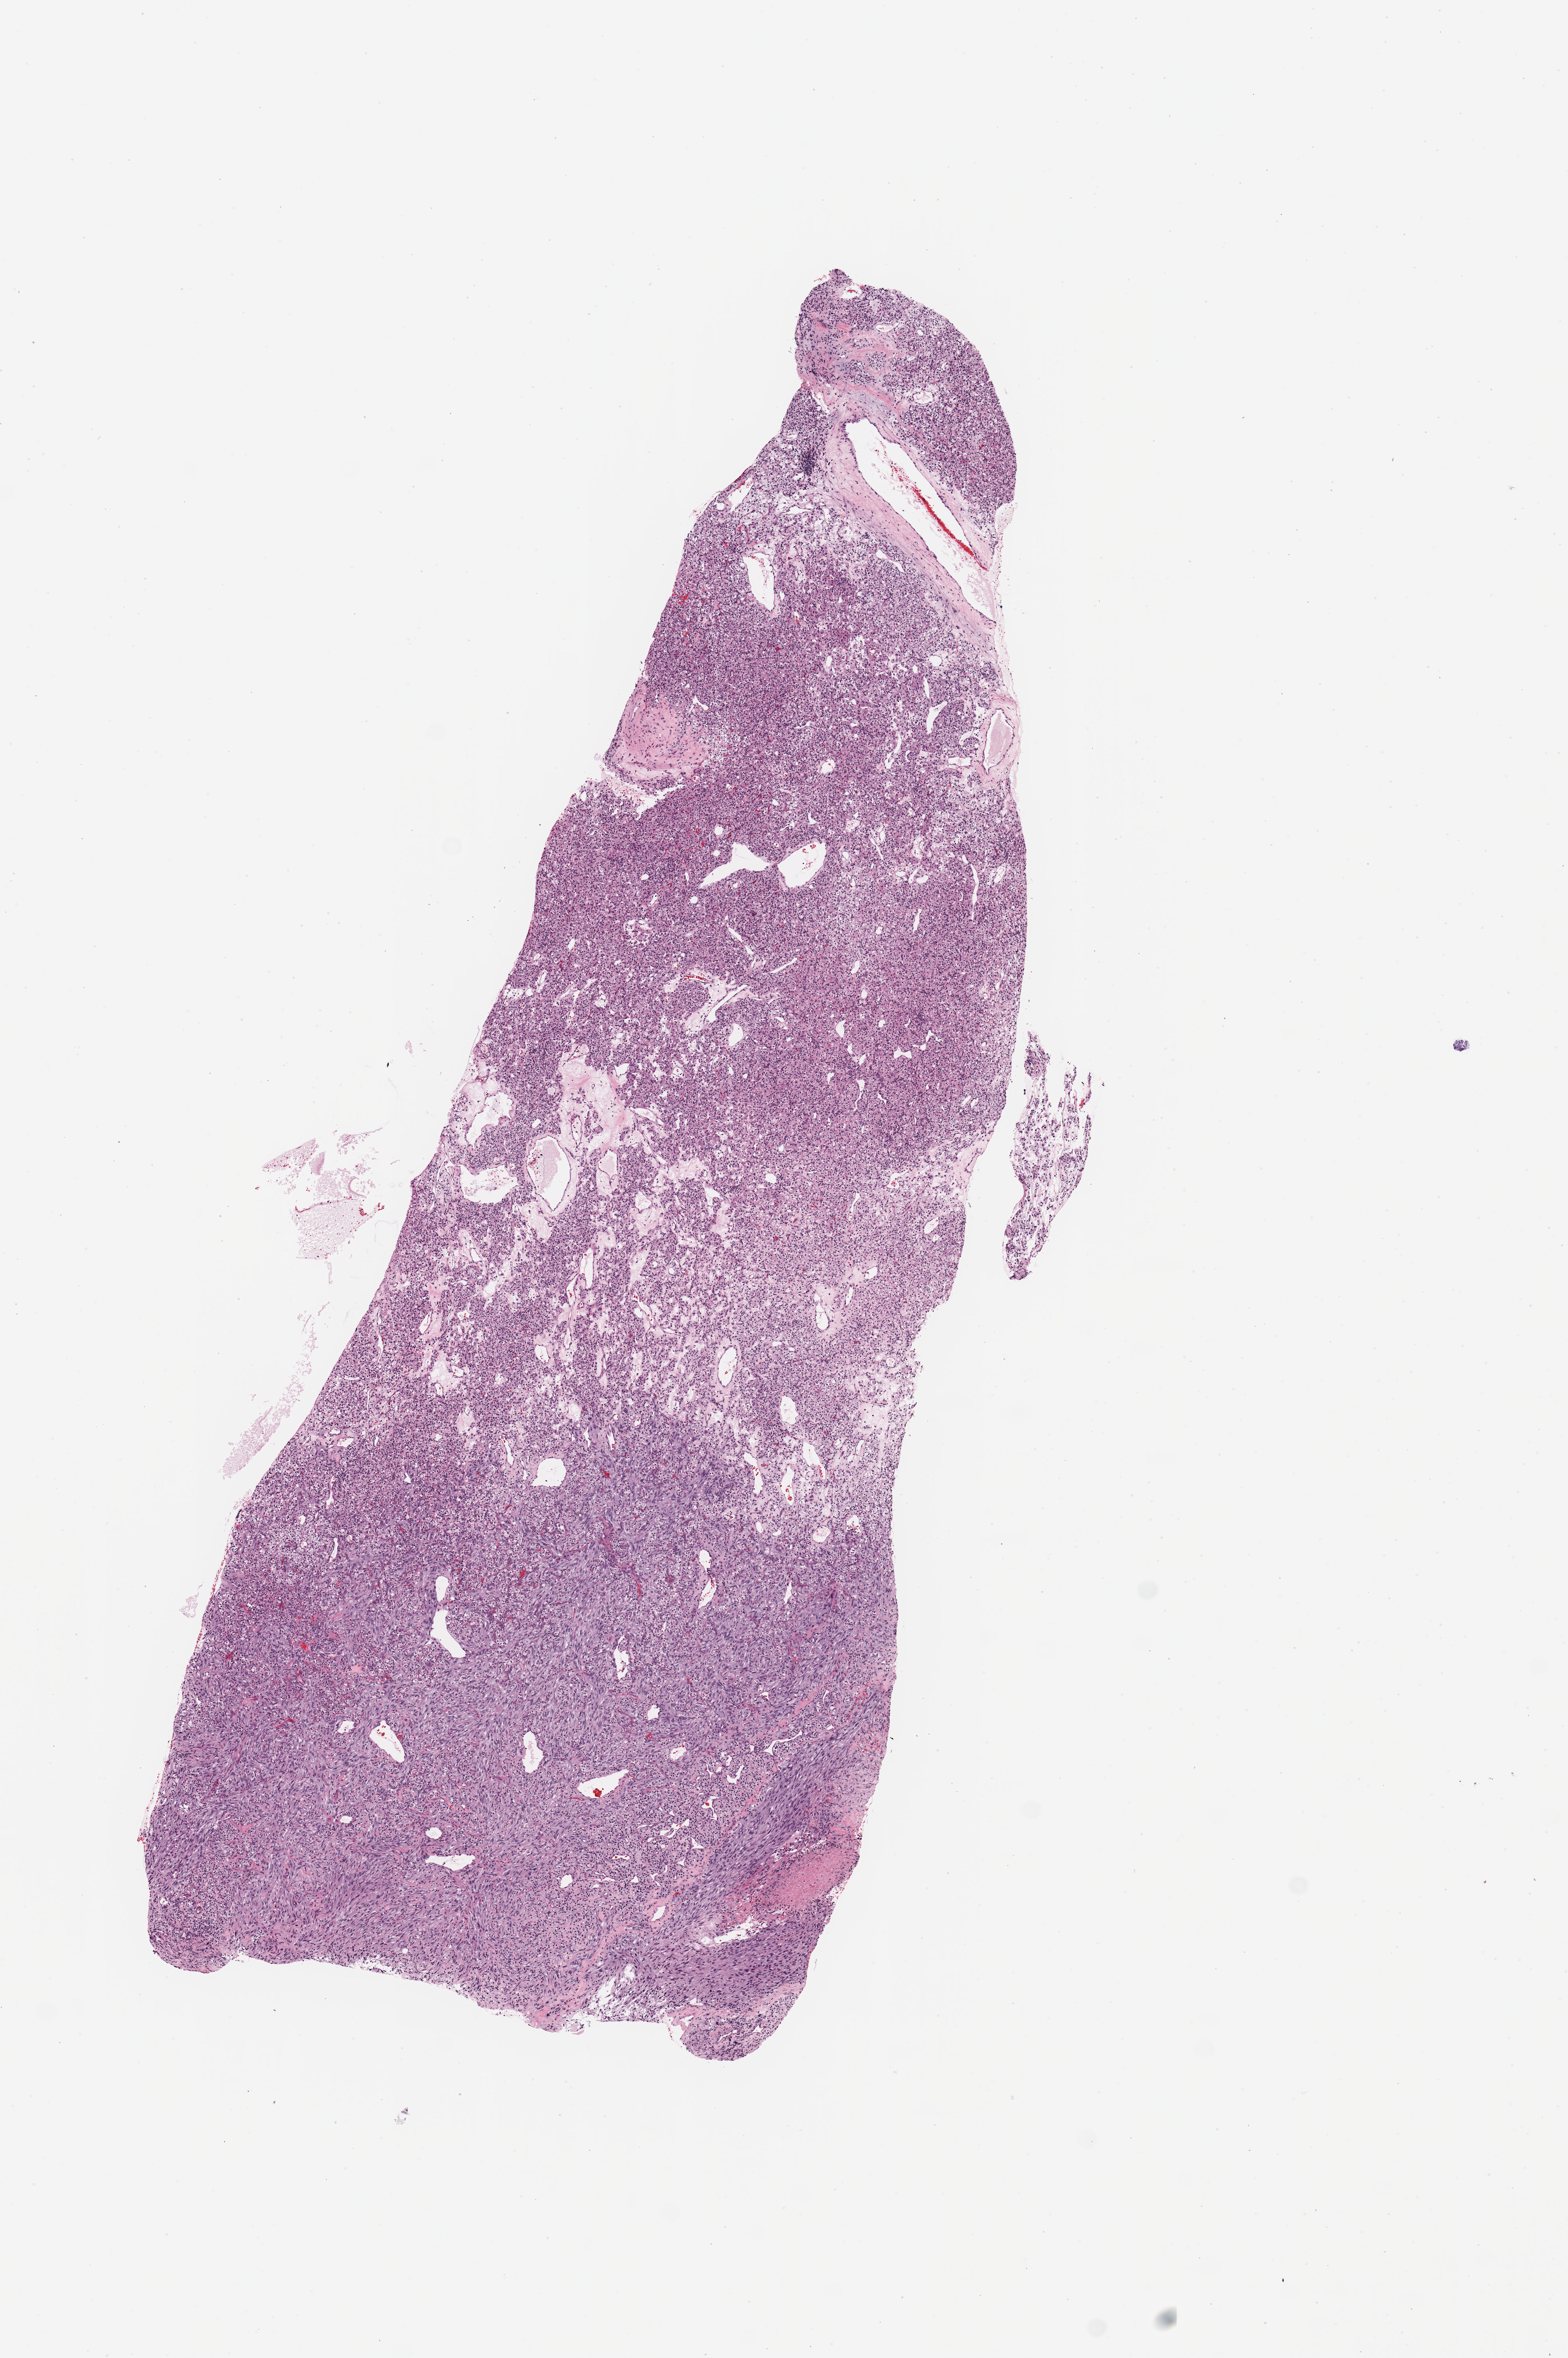
Whole-slide histology image, Hematoxylin and eosin (H&E) stained, shown as a low-resolution overview of the whole scanned area (about 7.9 x 11.8 mm, acquisition: 20x scan), tumour tissue sample, sampled site: kidney. 49-year-old male patient.
Diagnosis: Renal cell carcinoma, NOS.